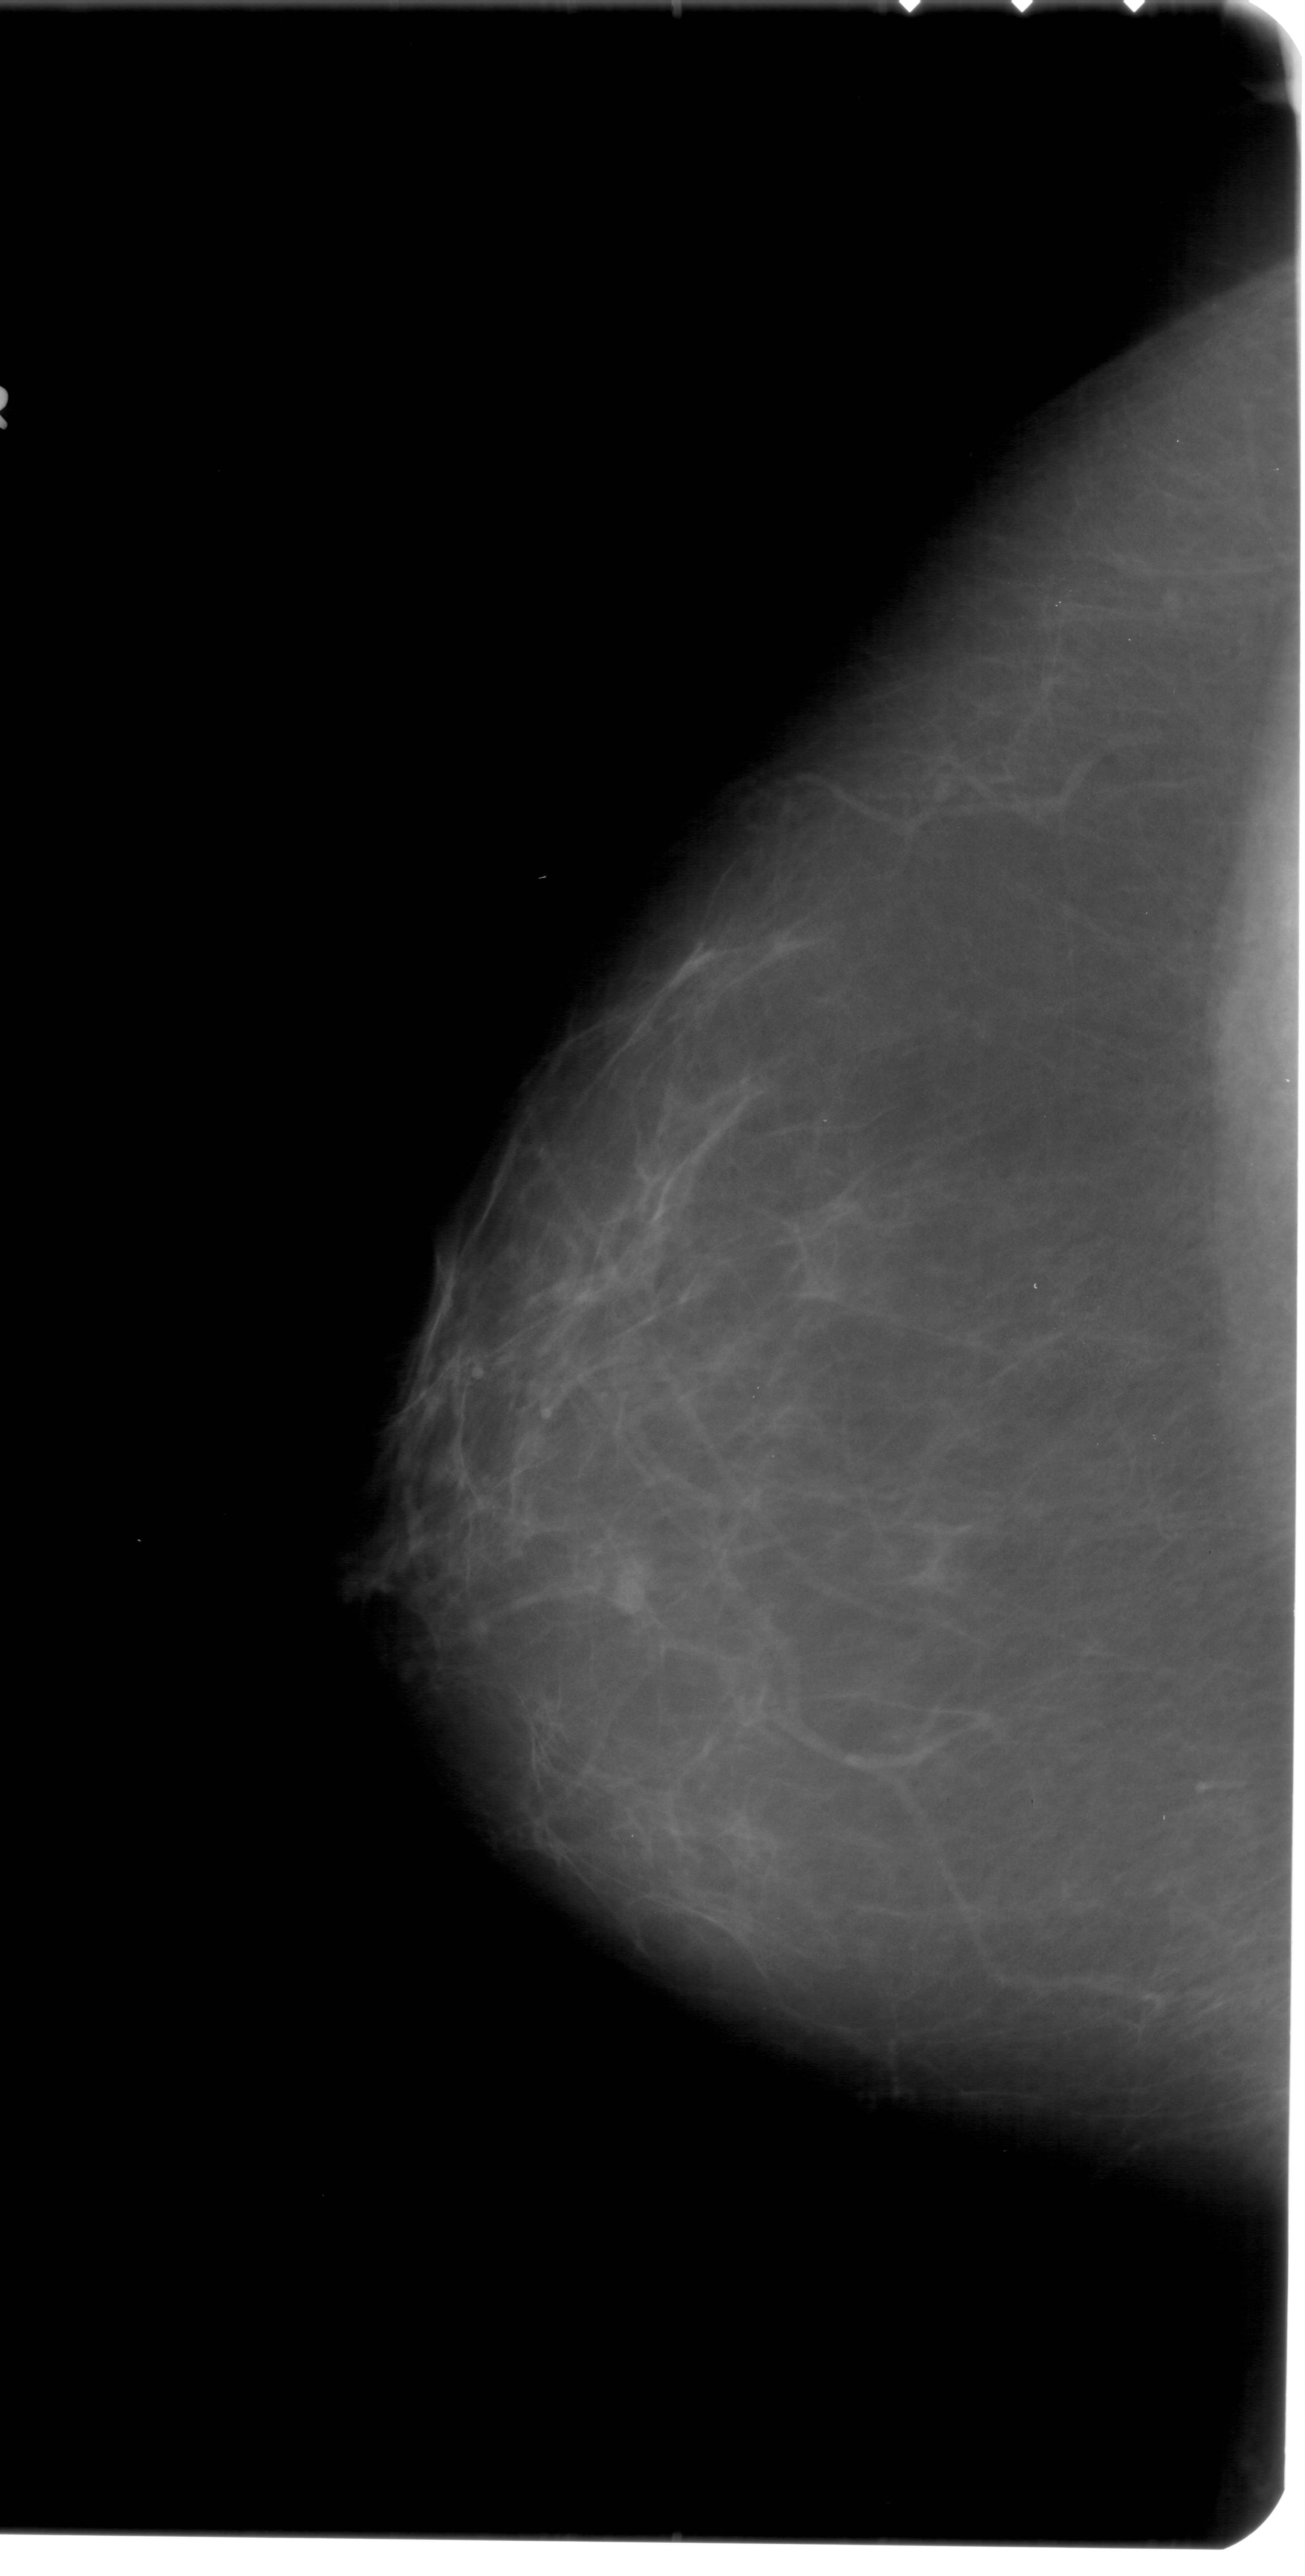
Scanned film-screen mammogram. Left breast. Craniocaudal (CC) view. Breast composition: scattered fibroglandular densities (BI-RADS density category 2 of 4). 1305 × 2576 image matrix.
Expert-marked regions of interest on this image (one box per marked abnormality):
- mass, shape lobulated, margins ill defined; BI-RADS assessment category 4; pathology result (as recorded, not read from the image): benign: bounding box (x1, y1, x2, y2) in pixels: (597, 1539, 673, 1639)